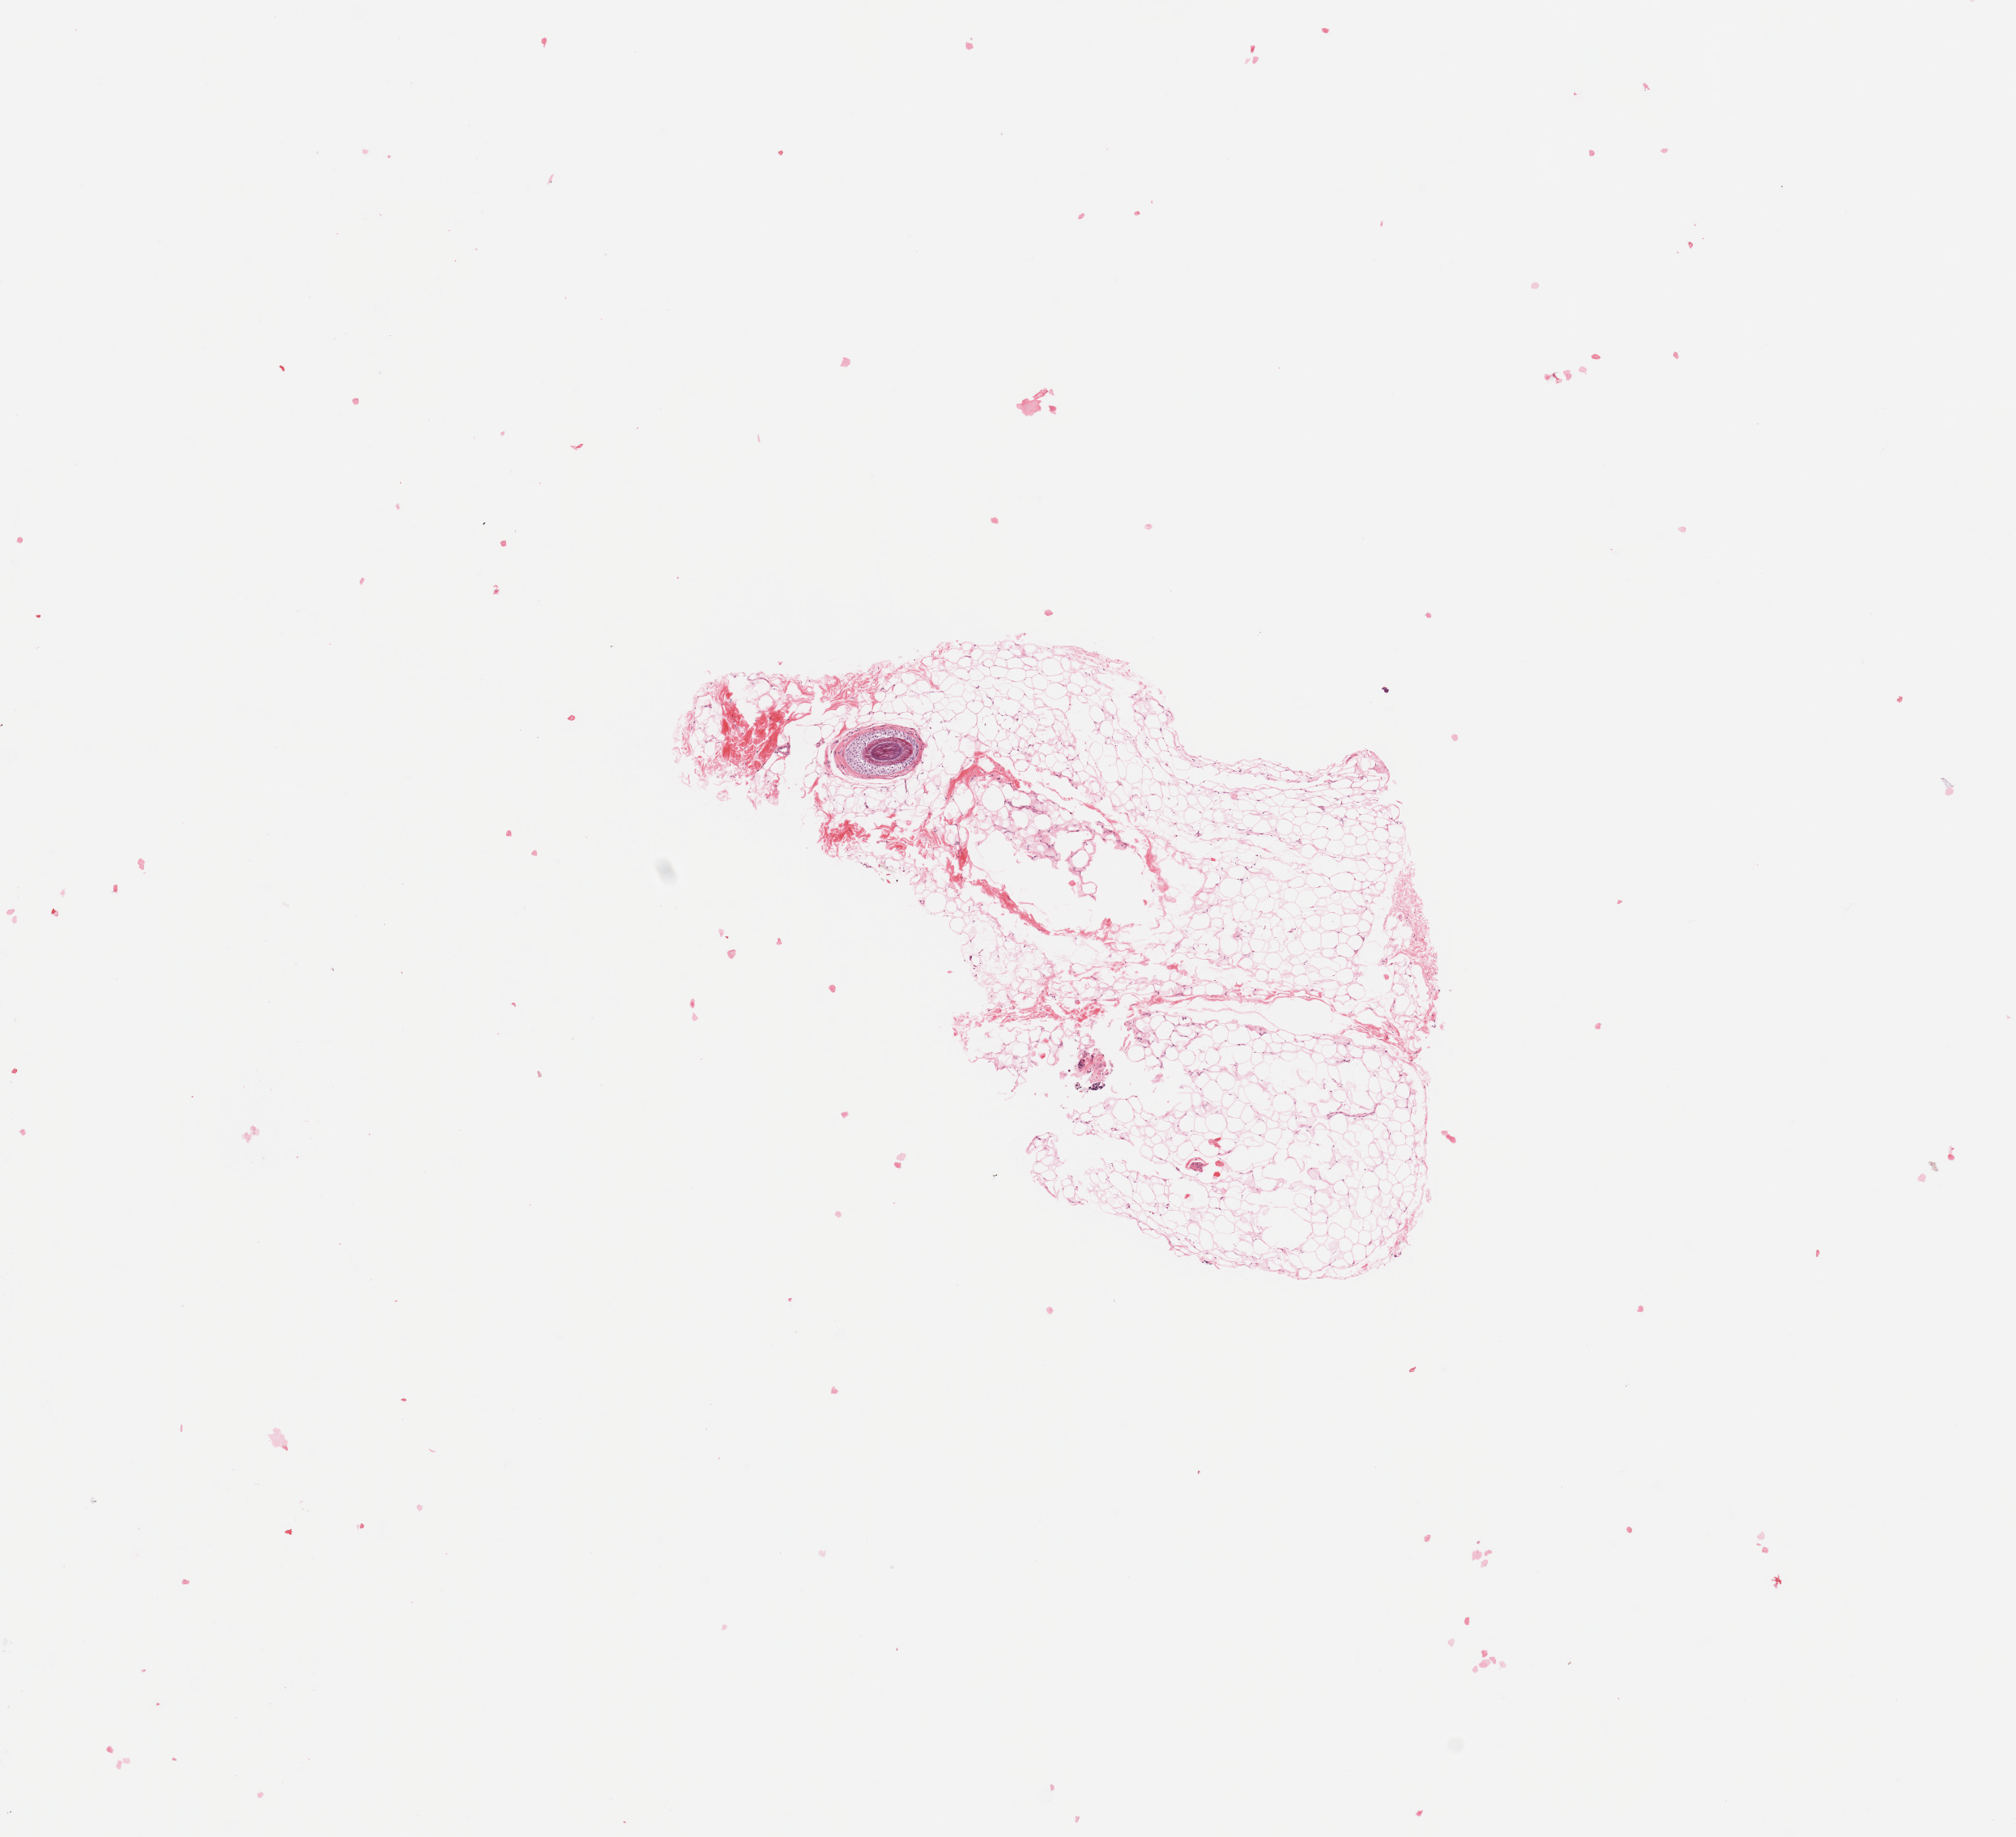
Digitized H&E tissue section (whole slide) — low-resolution overview of the scanned area, about 9.8 x 9.0 mm. Normal (non-tumour) tissue (melanoma cohort); sampled site not recorded. 73-year-old female patient.
This section: normal (non-tumour) tissue from the same patient. Patient diagnosis: Malignant melanoma, NOS.